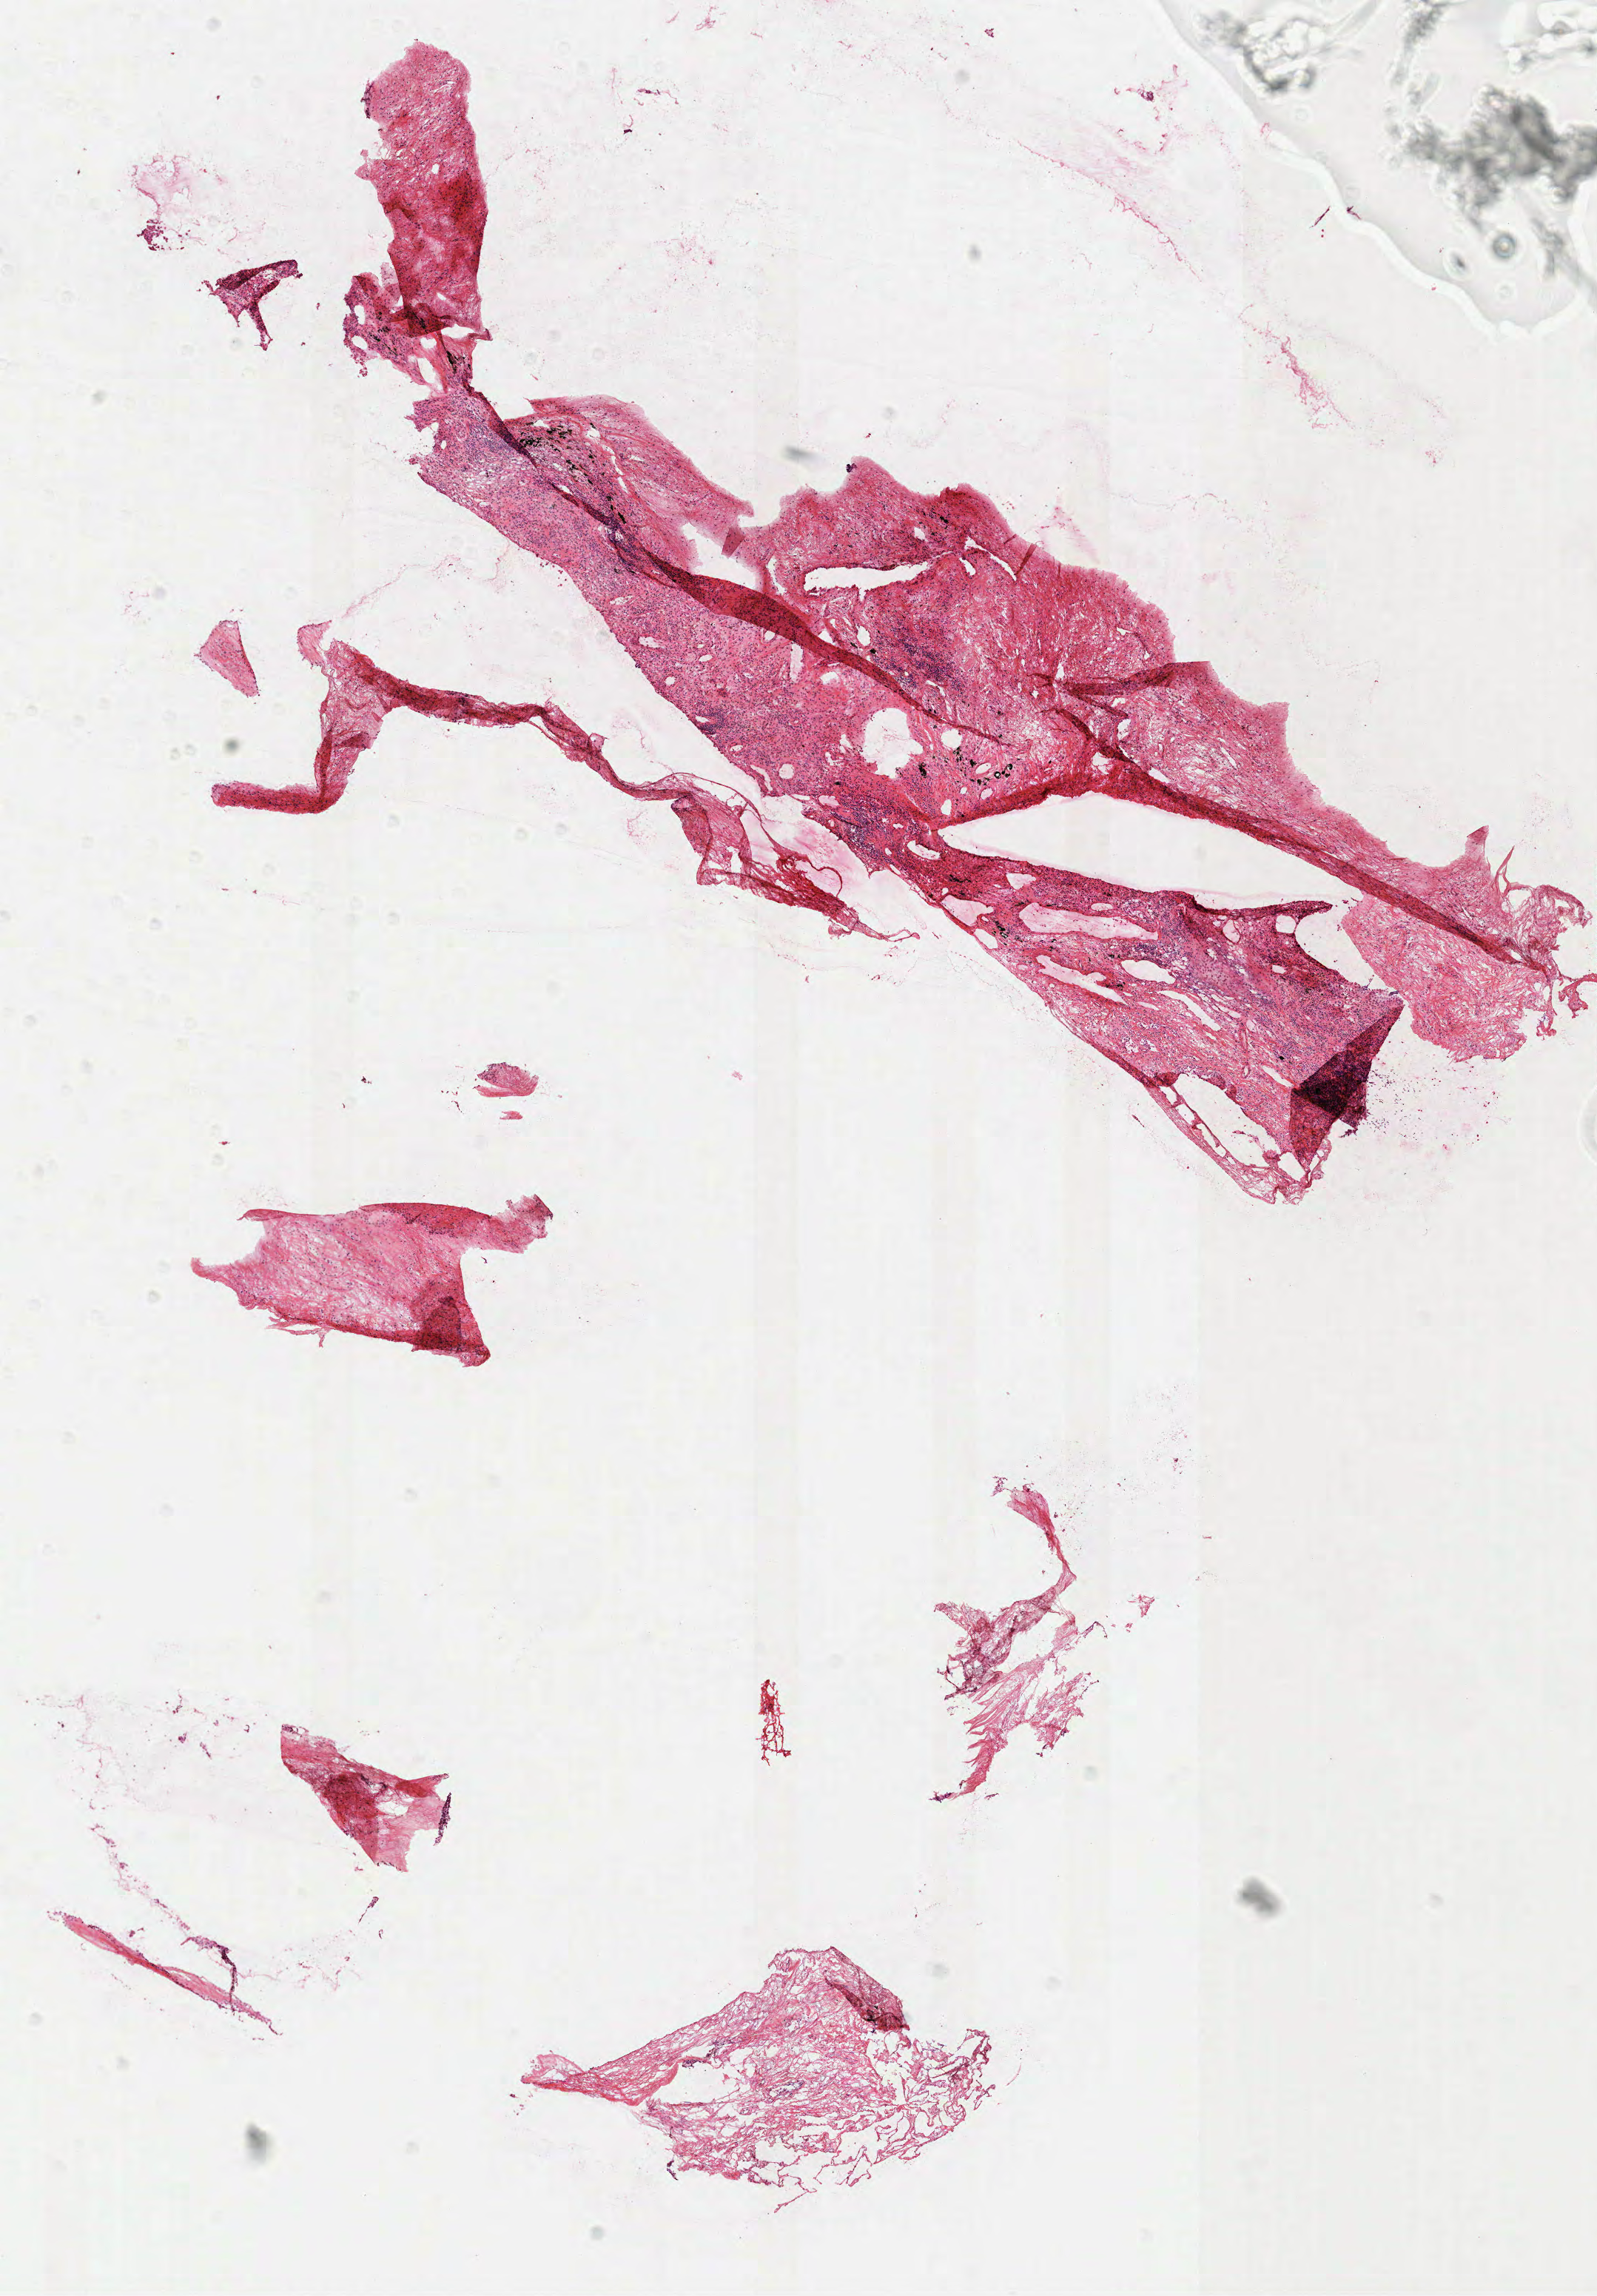
Whole-slide histology image, H&E, whole scanned area (about 8.7 x 12.5 mm, from a 40x scan) shown as a low-resolution overview; frozen section; lung, solid tissue normal (non-tumour tissue) sample. Patient: female, age at initial diagnosis 63 years.
This section: solid tissue normal (non-tumour) sample from the same patient. Patient diagnosis: Adenocarcinoma with mixed subtypes (upper lobe, lung).